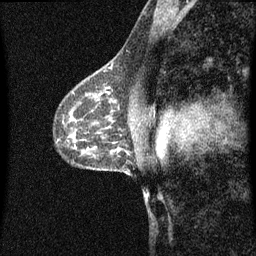
Breast MRI (dynamic contrast-enhanced), one sagittal slice; slice 44 of 60 in the series (ordered by position); dynamic contrast-enhanced series, image 2 of 3 at this slice position (ordered by acquisition); 1.5 T; TE 4.2 ms, TR 8.4 ms; 2 mm slice thickness; 256 × 256 image matrix, field of view 200 × 200 mm. Patient: female, 41 years.
Outlined on this slice (semi-automatic segmentation, software-assisted and operator-edited):
- analysis volume of interest (the breast-tissue region the enhancement analysis was run in; not a lesion): bounding box [x1, y1, x2, y2] px = [94, 72, 119, 97]
- tumour enhancement mask (voxels above the 70 % enhancement threshold inside the analysis volume of interest): [100, 86, 111, 95]